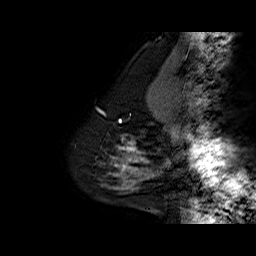
Breast MRI (dynamic contrast-enhanced), one sagittal slice. Slice 13 of 60 in the series (ordered by position). Dynamic contrast-enhanced series, time point 2 of 6 at this slice position (early post-contrast). 1.5 T. TE 6.3 ms, TR 32.5 ms. 4 mm slice thickness. 256 × 256 image matrix. Female patient. Case-level facts recorded for this patient, not image findings: setting: breast cancer imaged before/during neoadjuvant chemotherapy; receptor status: triple-negative.
Annotated regions visible in this slice (semi-automatic segmentation, software-assisted and operator-edited):
- analysis volume of interest (the breast-tissue region the enhancement analysis was run in; not a lesion): bounding box (x1, y1, x2, y2) in pixels: (108, 134, 154, 177)
- tumour enhancement mask (voxels above the 100 % enhancement threshold inside the analysis volume of interest): (118, 141, 148, 171)